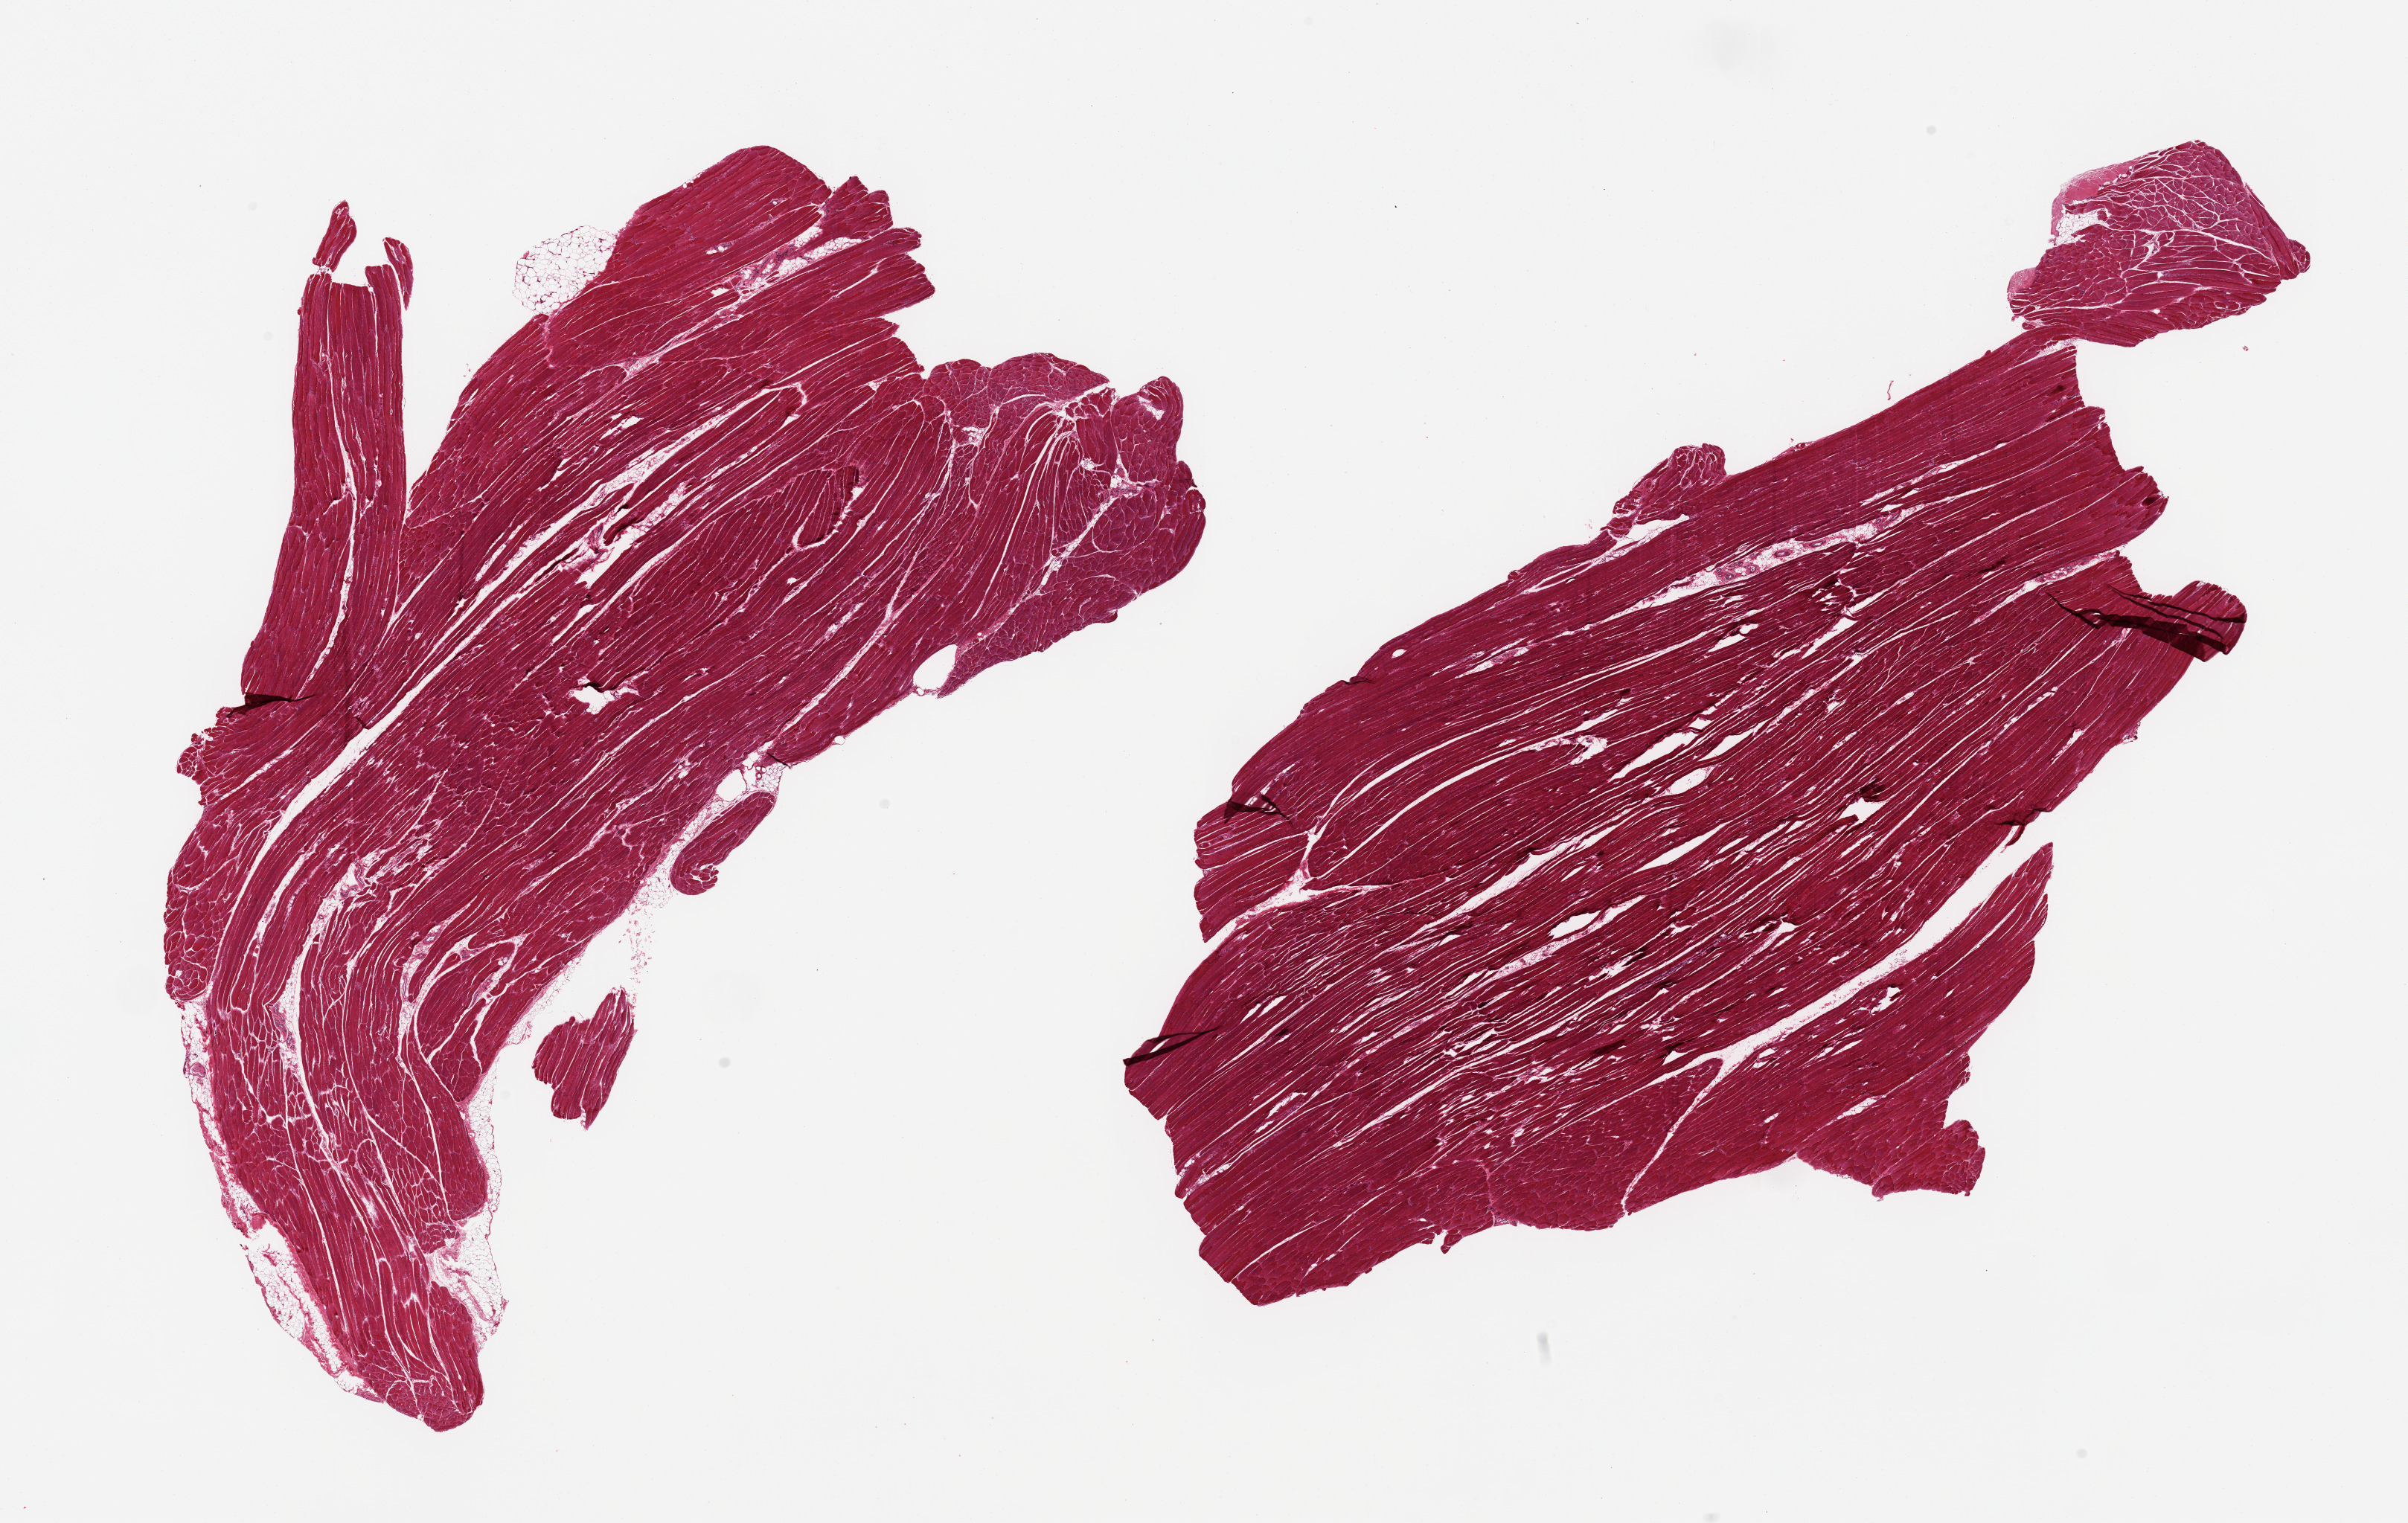
Digitized hematoxylin and eosin (H&E)-stained section, a low-resolution overview of the entire scanned area, about 25.6 x 16.2 mm (from a 20x scan); PAXgene-fixed paraffin-embedded (PFPE) section; target tissue: skeletal muscle; tissue donor sample. Female donor.
Review note (as recorded): 2 pieces; includes minimal portion of fat.